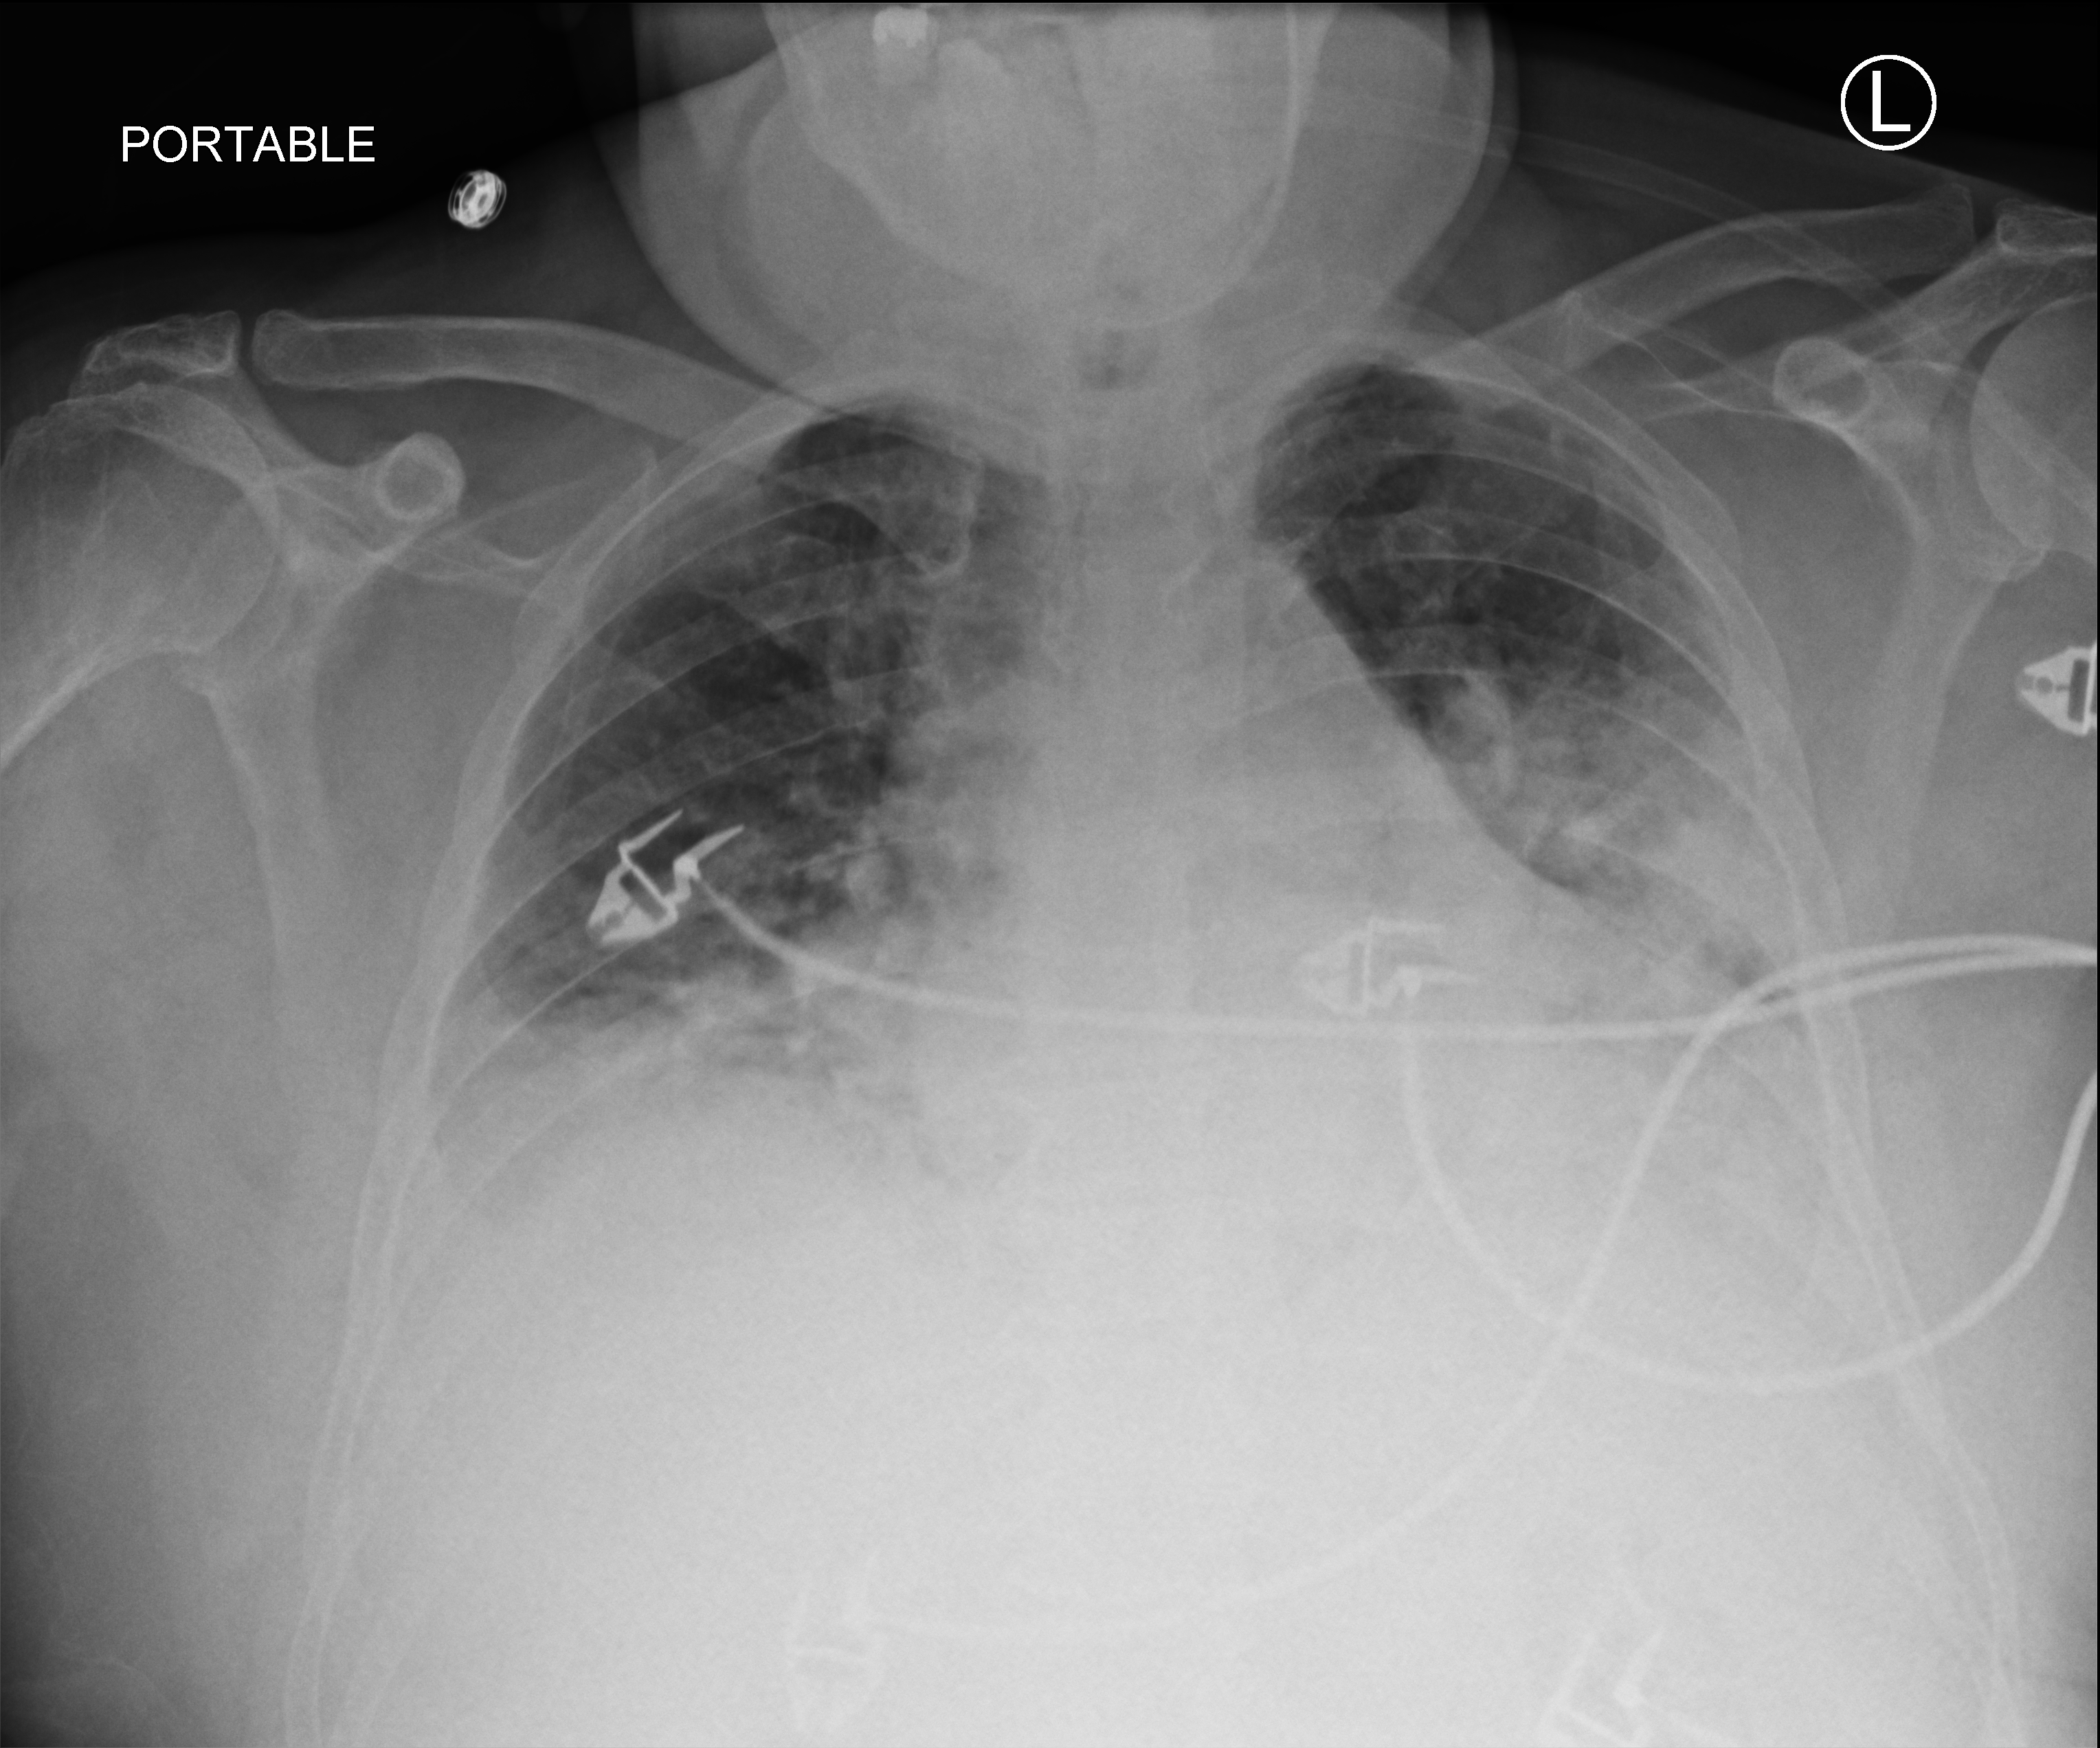
Portable chest radiograph, anteroposterior (AP) projection. Patient hospitalised with COVID-19; male, aged 60–74 years.
Hospital-stay facts (about this admission, not read from this image; timing relative to this image not recorded): diabetes (admission record): no; mechanically ventilated during this hospital stay: yes.